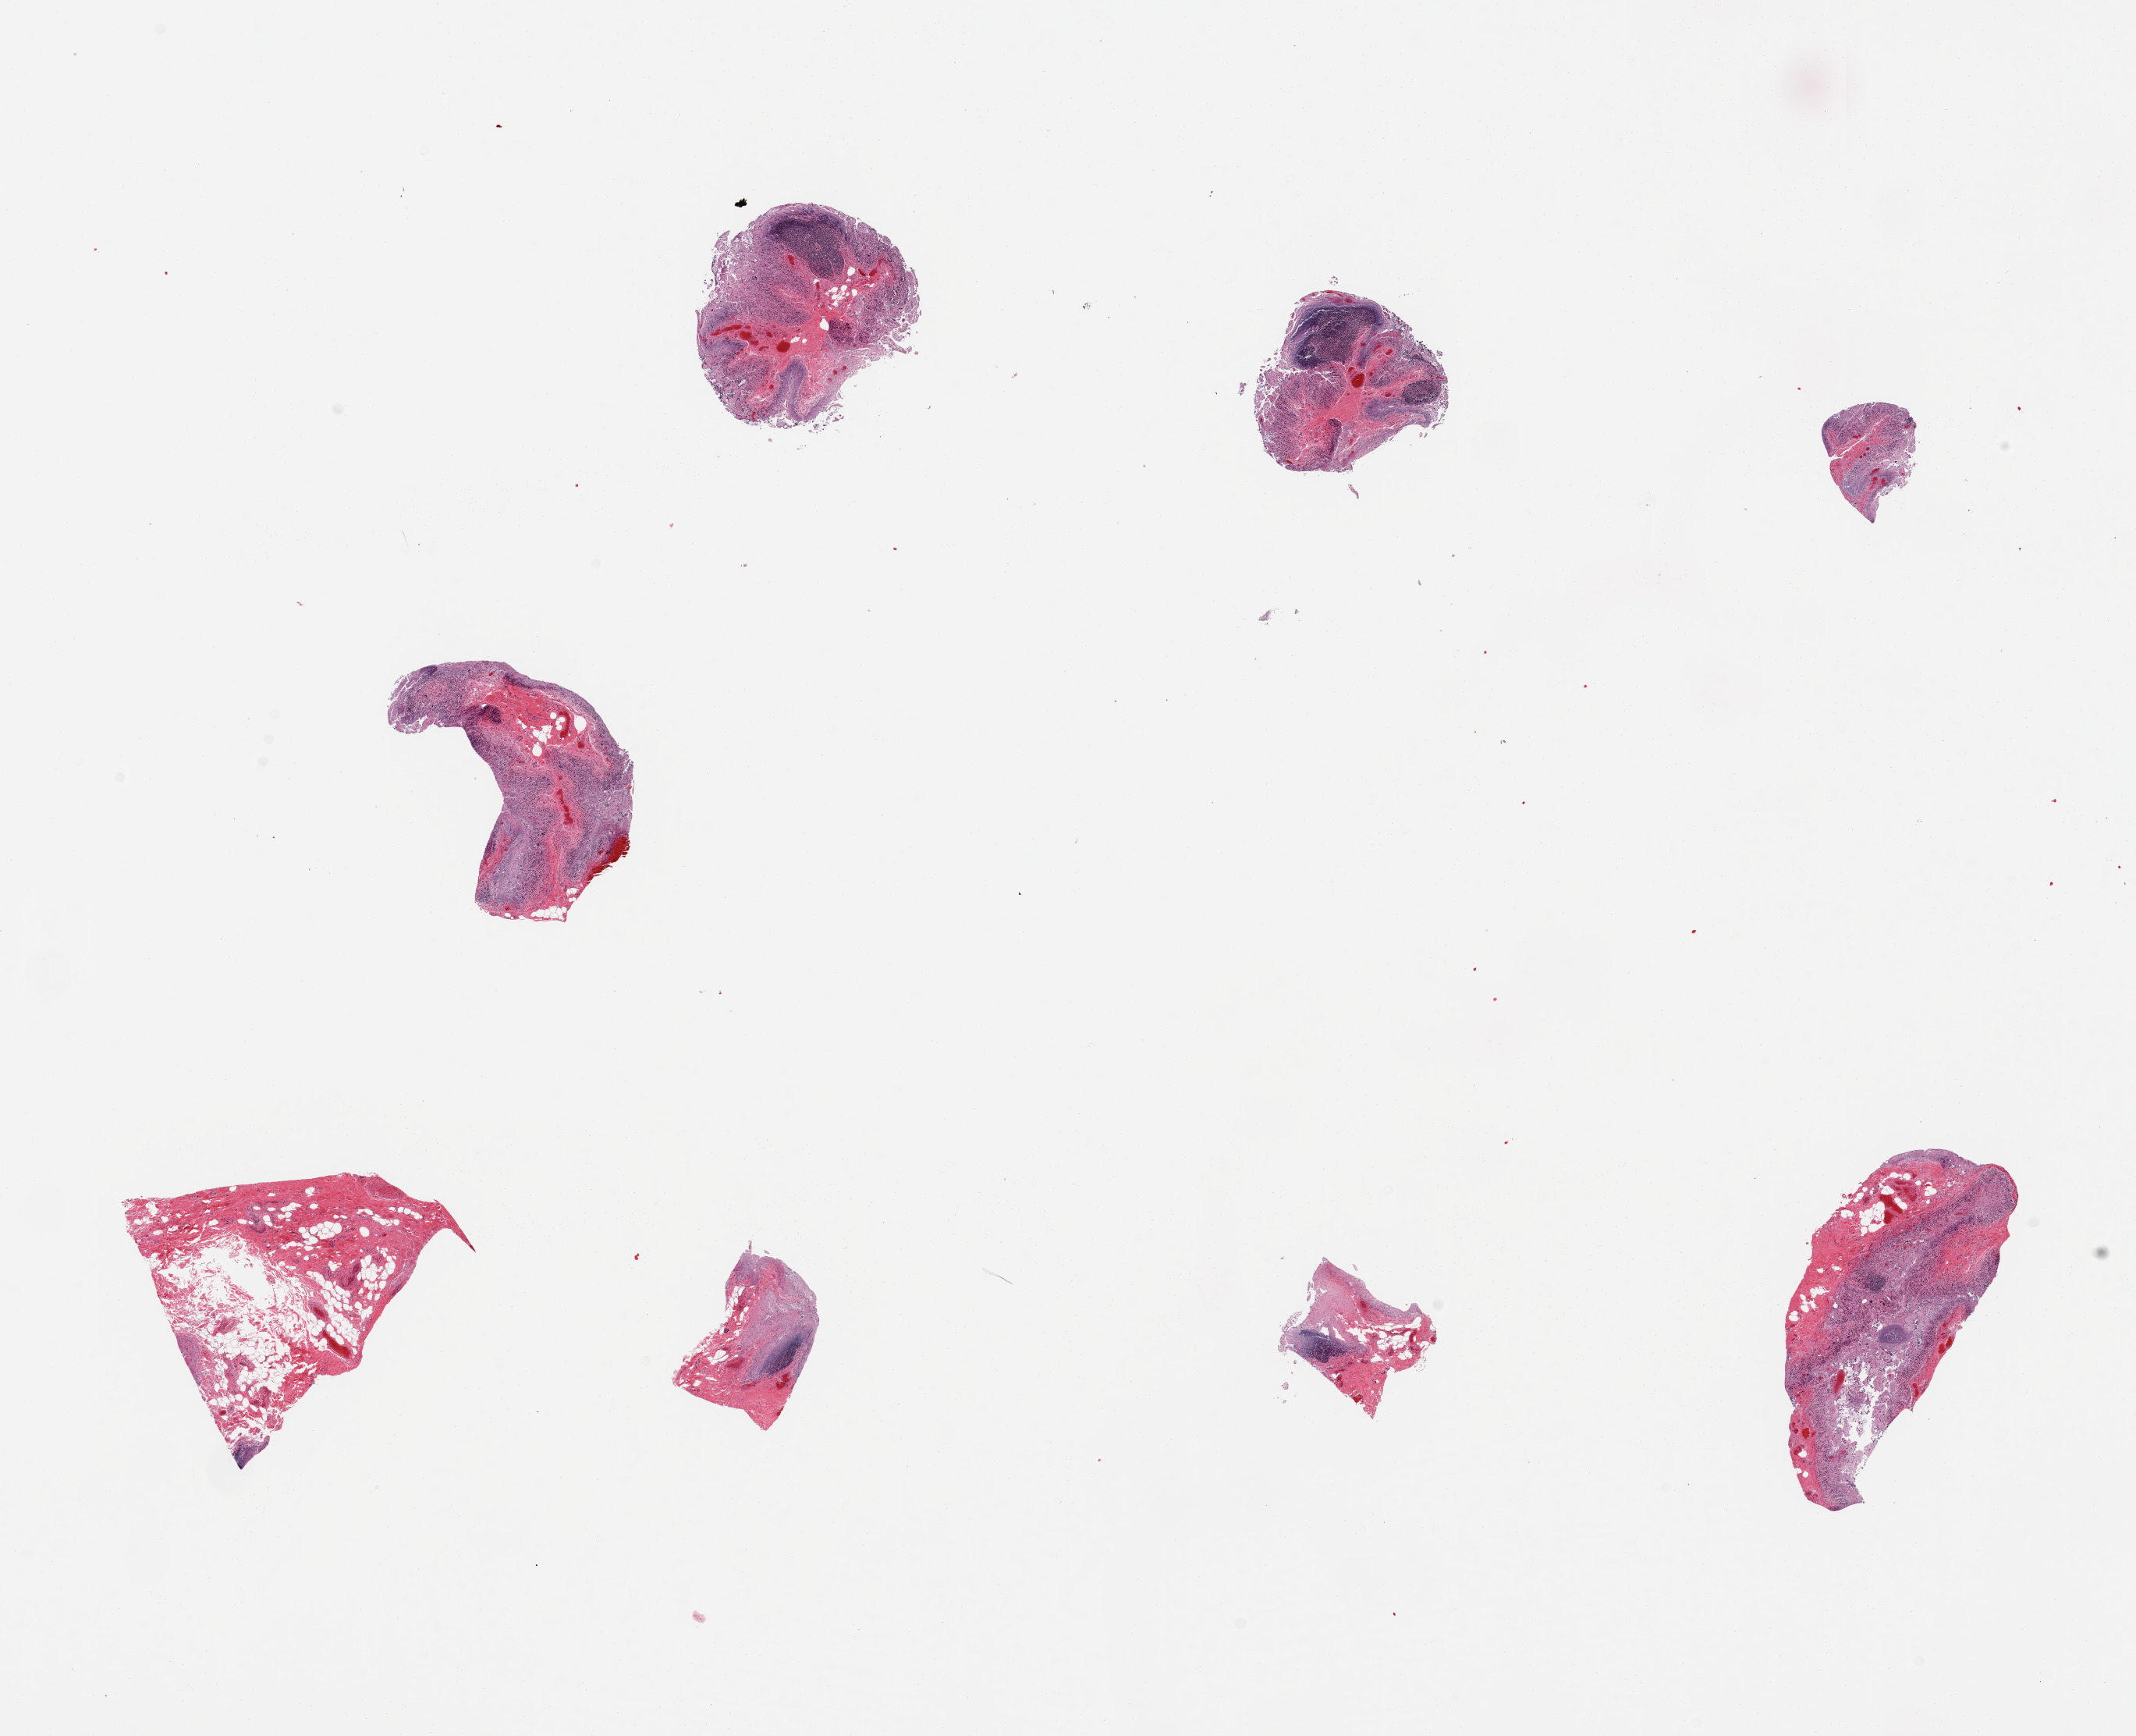
Haematoxylin and eosin whole-slide image, brightfield — whole scanned area (about 21.7 x 17.6 mm, from a 20x scan) shown as a low-resolution overview. Male donor.
Specimen: PAXgene-fixed paraffin-embedded (PFPE) section; target tissue: ileum; donor tissue sample.